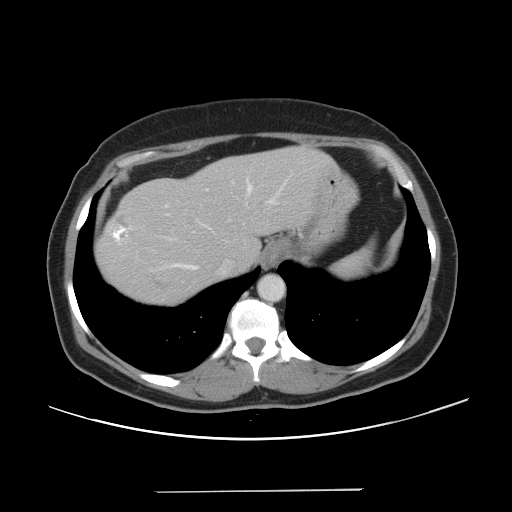
Contrast-enhanced abdominal CT, one axial slice. Slice 38 of 56 in the series (ordered by position). Intravenous contrast given. Soft-tissue window (W 400 / L 40 HU). 5 mm slice thickness. 512 × 512 image matrix, field of view 419 × 419 mm. Female patient, age 54 years. Case-level facts recorded for this patient, not image findings: diagnosis: colorectal cancer liver metastases, imaged before liver resection; multiple liver metastases: yes; largest metastasis: 3.2 cm; chemotherapy before resection: yes.
Structures marked on this image (manually delineated by an expert):
- hepatic veins: bounding box <135,177,287,272> (left, top, right, bottom; pixels)
- liver: <96,147,334,308>
- planned liver remnant (the part of the liver to remain after resection): <196,147,333,273>
- liver metastasis: <153,273,167,288>
- liver metastasis: <109,215,129,241>
- liver metastasis: <188,217,195,224>